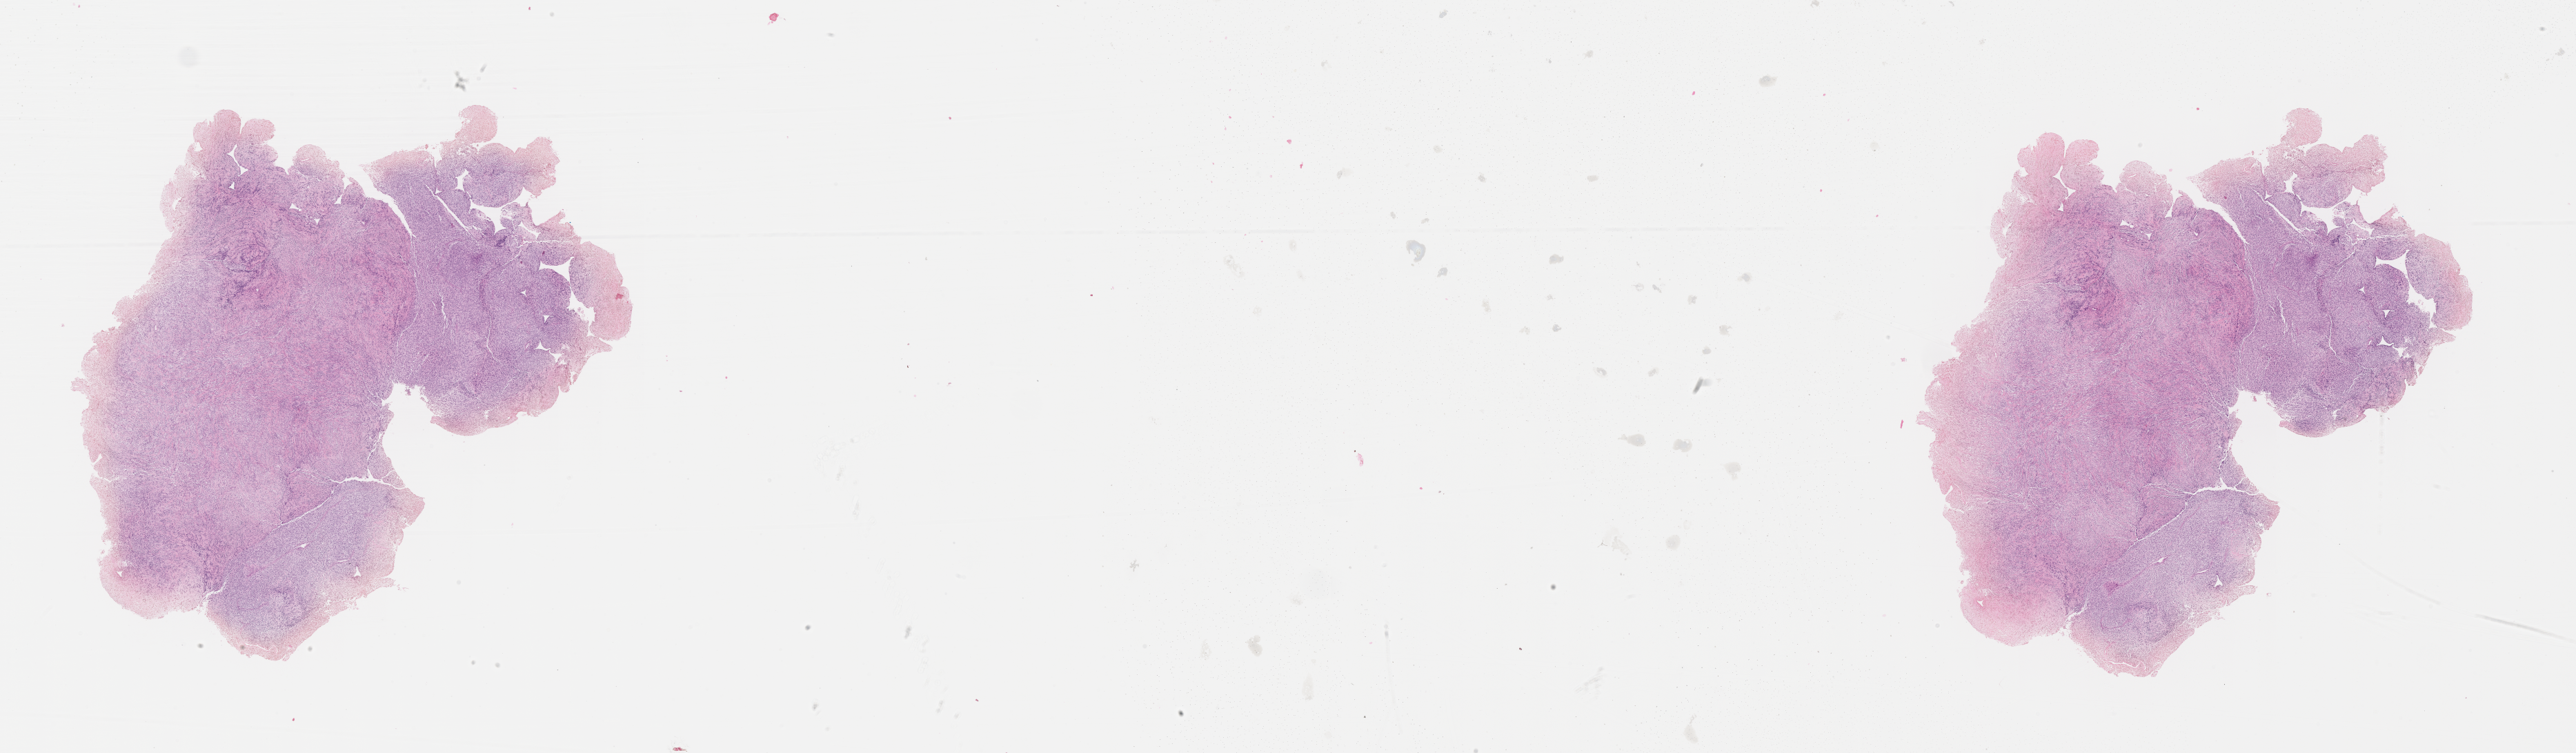
Haematoxylin and eosin whole-slide image of tumor tissue — whole scanned area (about 30.2 x 8.8 mm) shown as a low-resolution overview; FFPE section. Female patient, age at diagnosis 14.4 years.
Diagnosis: rhabdomyosarcoma; histological classification: spindle cell rhabdomyosarcoma.